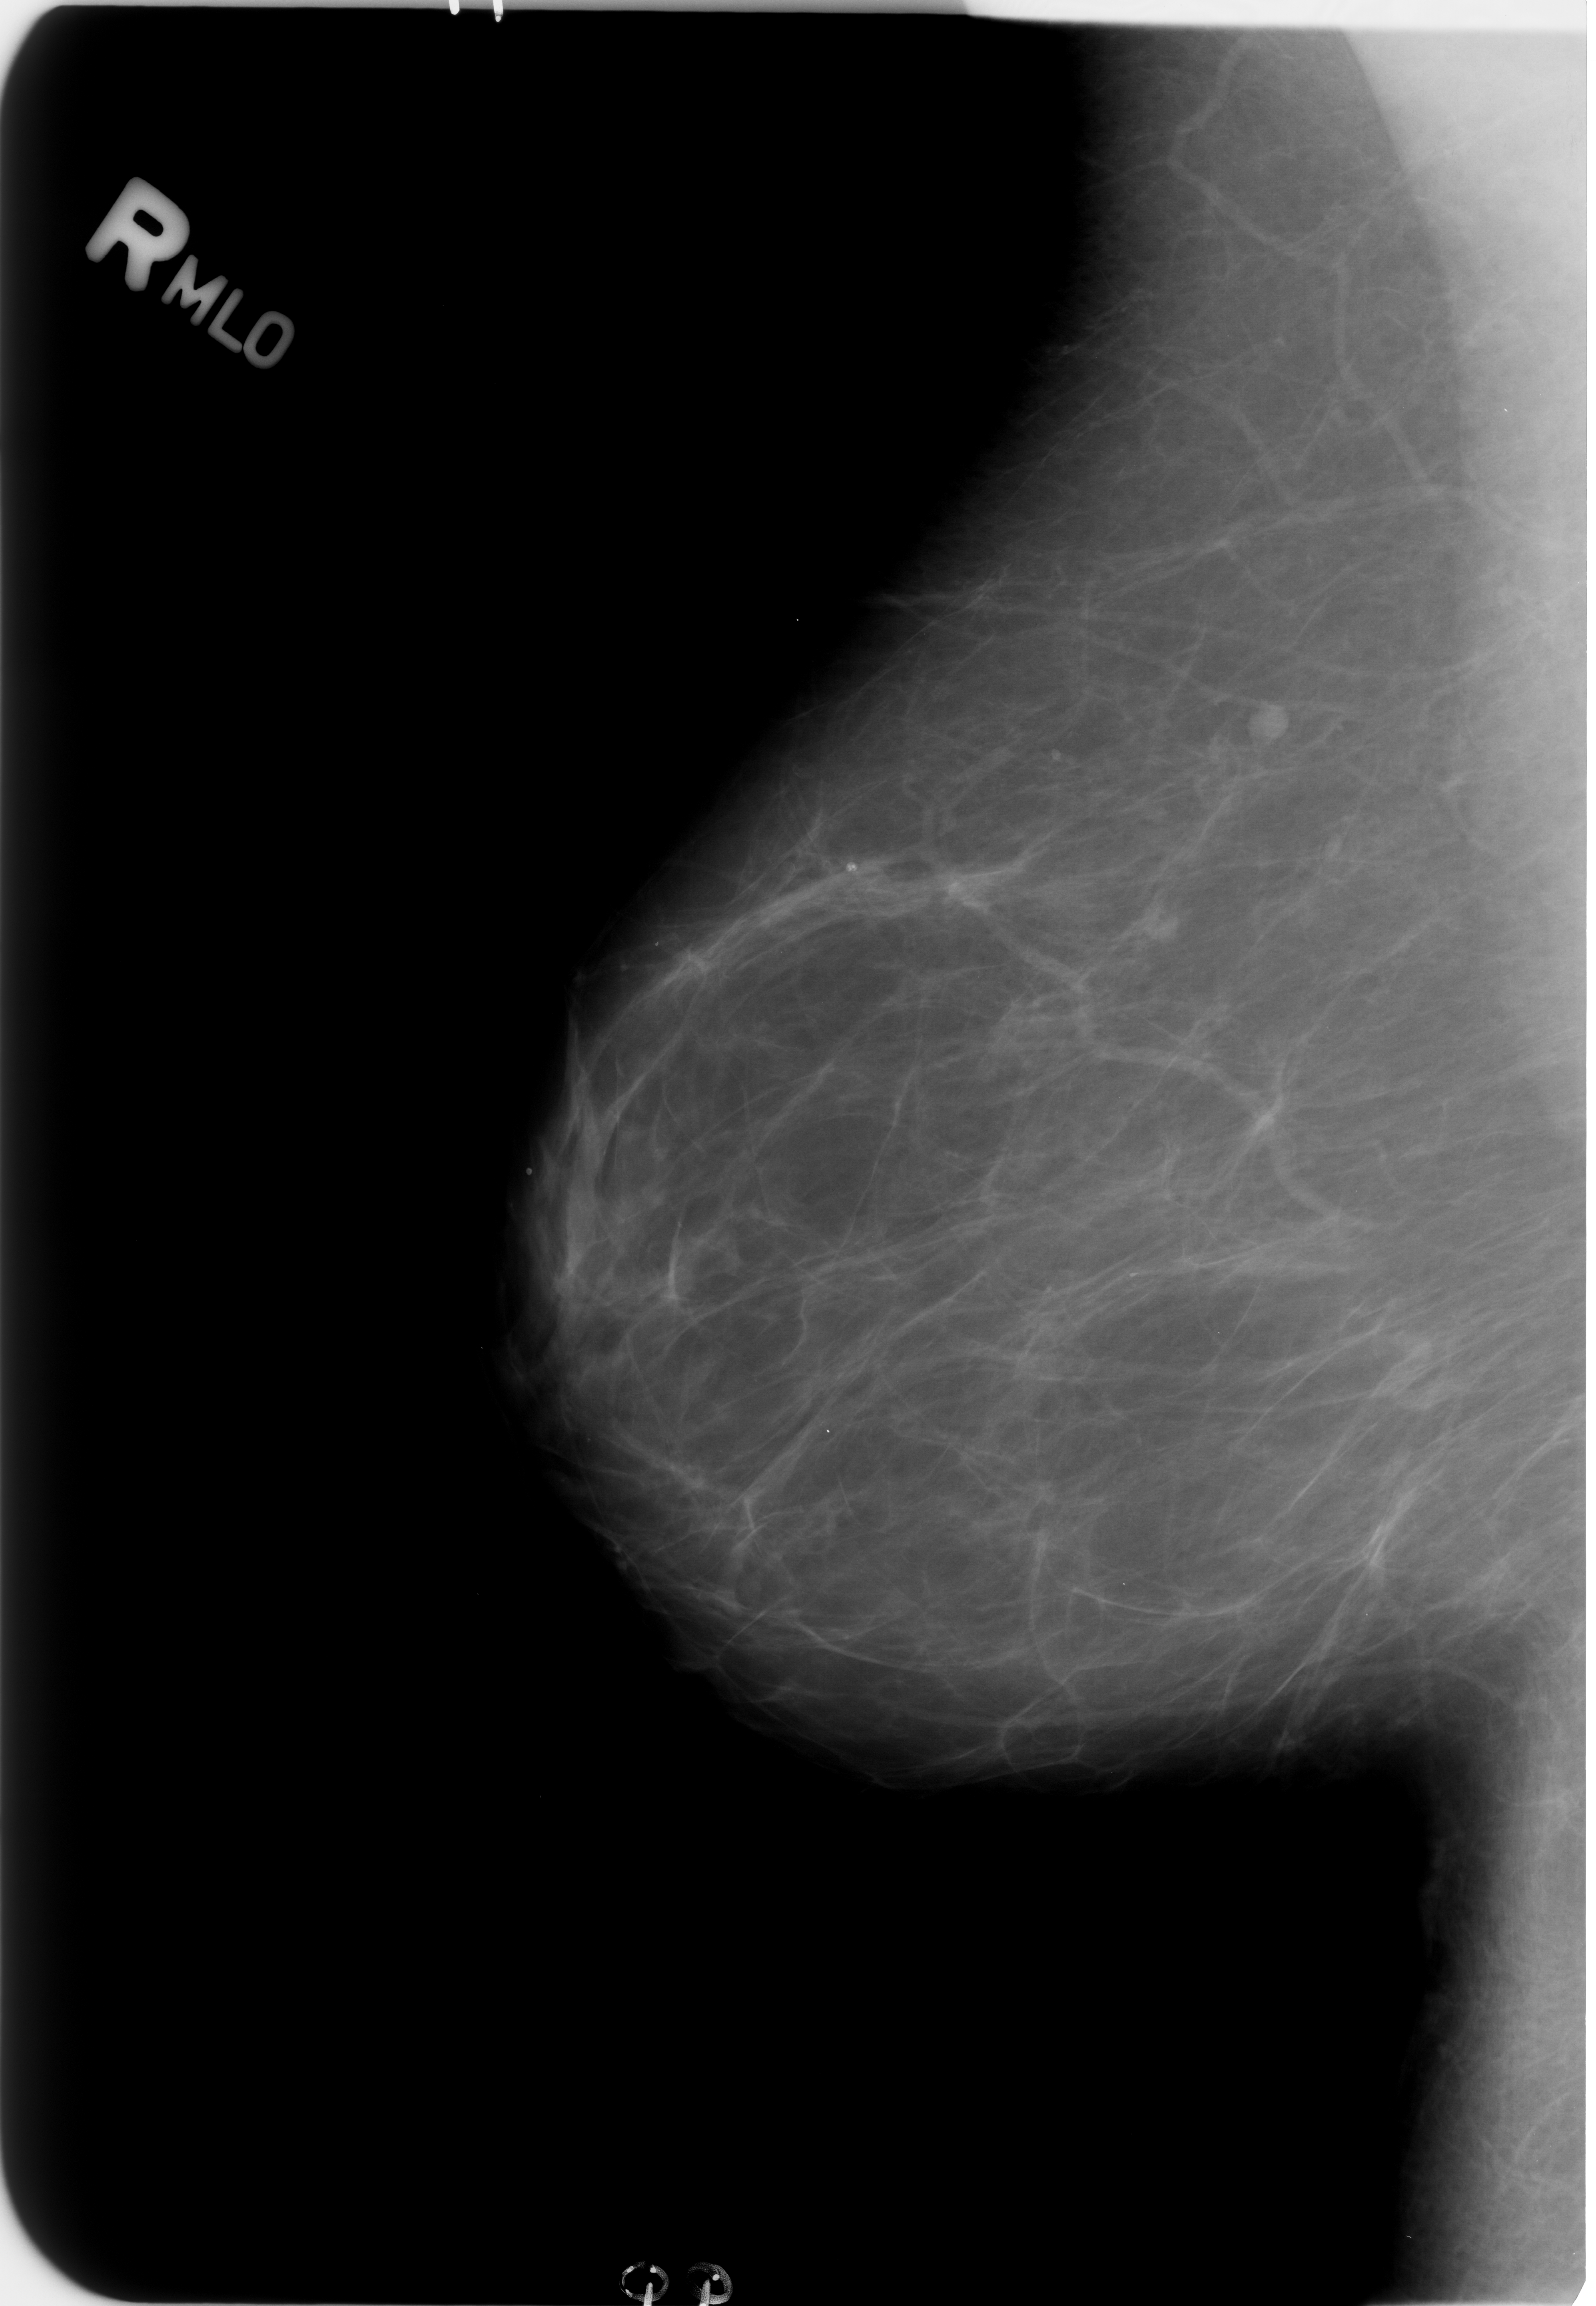
Digitized screen-film mammogram; right breast; MLO view.
Marked abnormality: calcifications, morphology coarse; BI-RADS assessment category 2; subtlety rating 4 on a 1 (subtle) to 5 (obvious) scale; benign; no additional work-up was recommended (benign without callback).